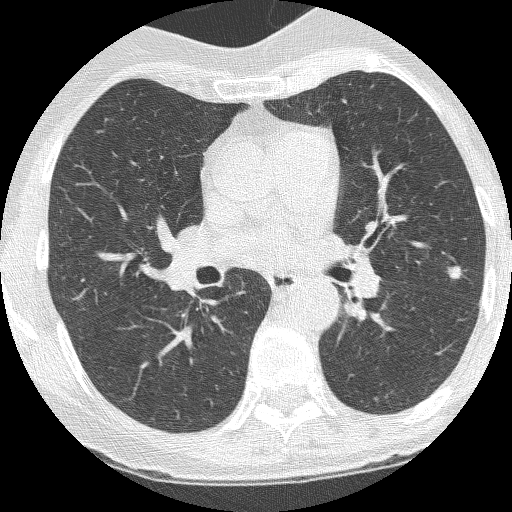
Low-dose screening chest CT, axial slice; third annual screen; lung window (W 1500 / L -600 HU); 1.25 mm slice thickness; lung (sharp) reconstruction kernel (BONE); 512 × 512 image matrix, field of view 251 × 251 mm. Female participant, aged 60 years at enrolment. Current smoker at enrolment.
• Lesion marked by an expert reader, bounding box (x1, y1, x2, y2) in pixels: (435, 259, 472, 293).
• The screening reader recorded 2 non-calcified nodules or masses ≥4 mm on this exam (left upper lobe, left upper lobe); which of them this box marks is not recorded.